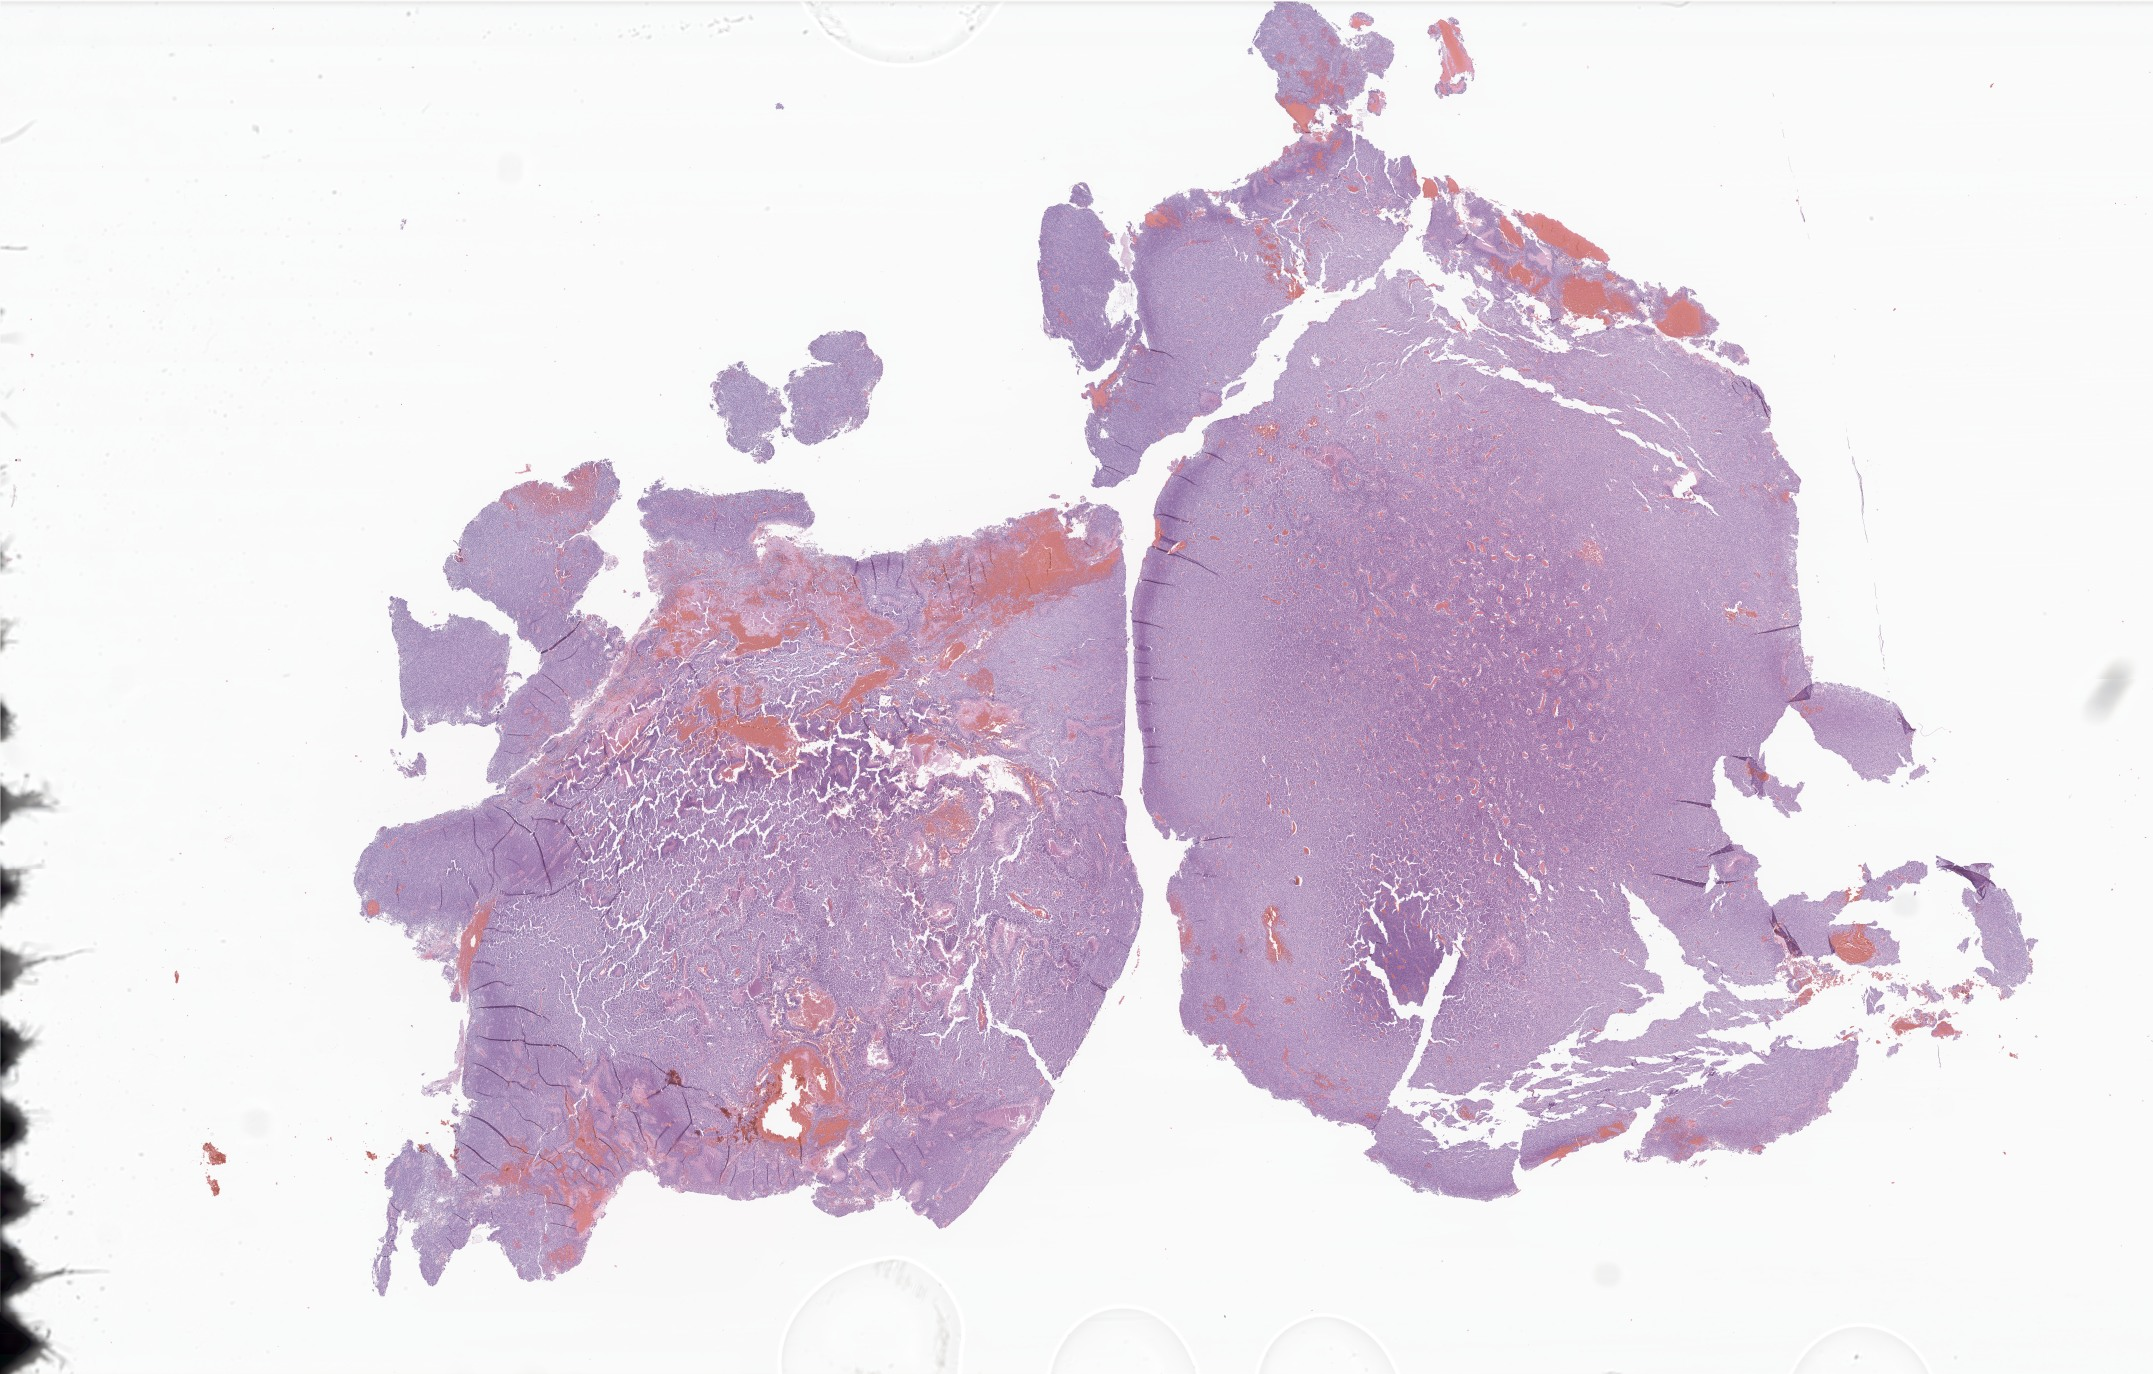
Whole-slide image, haematoxylin and eosin stain of tumor tissue from the brain, shown as a low-resolution overview of the whole scanned area (about 36.3 x 23.2 mm); formalin-fixed, paraffin-embedded (FFPE) tissue. Patient male; age 166 months (13 years 10 months).
* diagnosis: Glioma, malignant